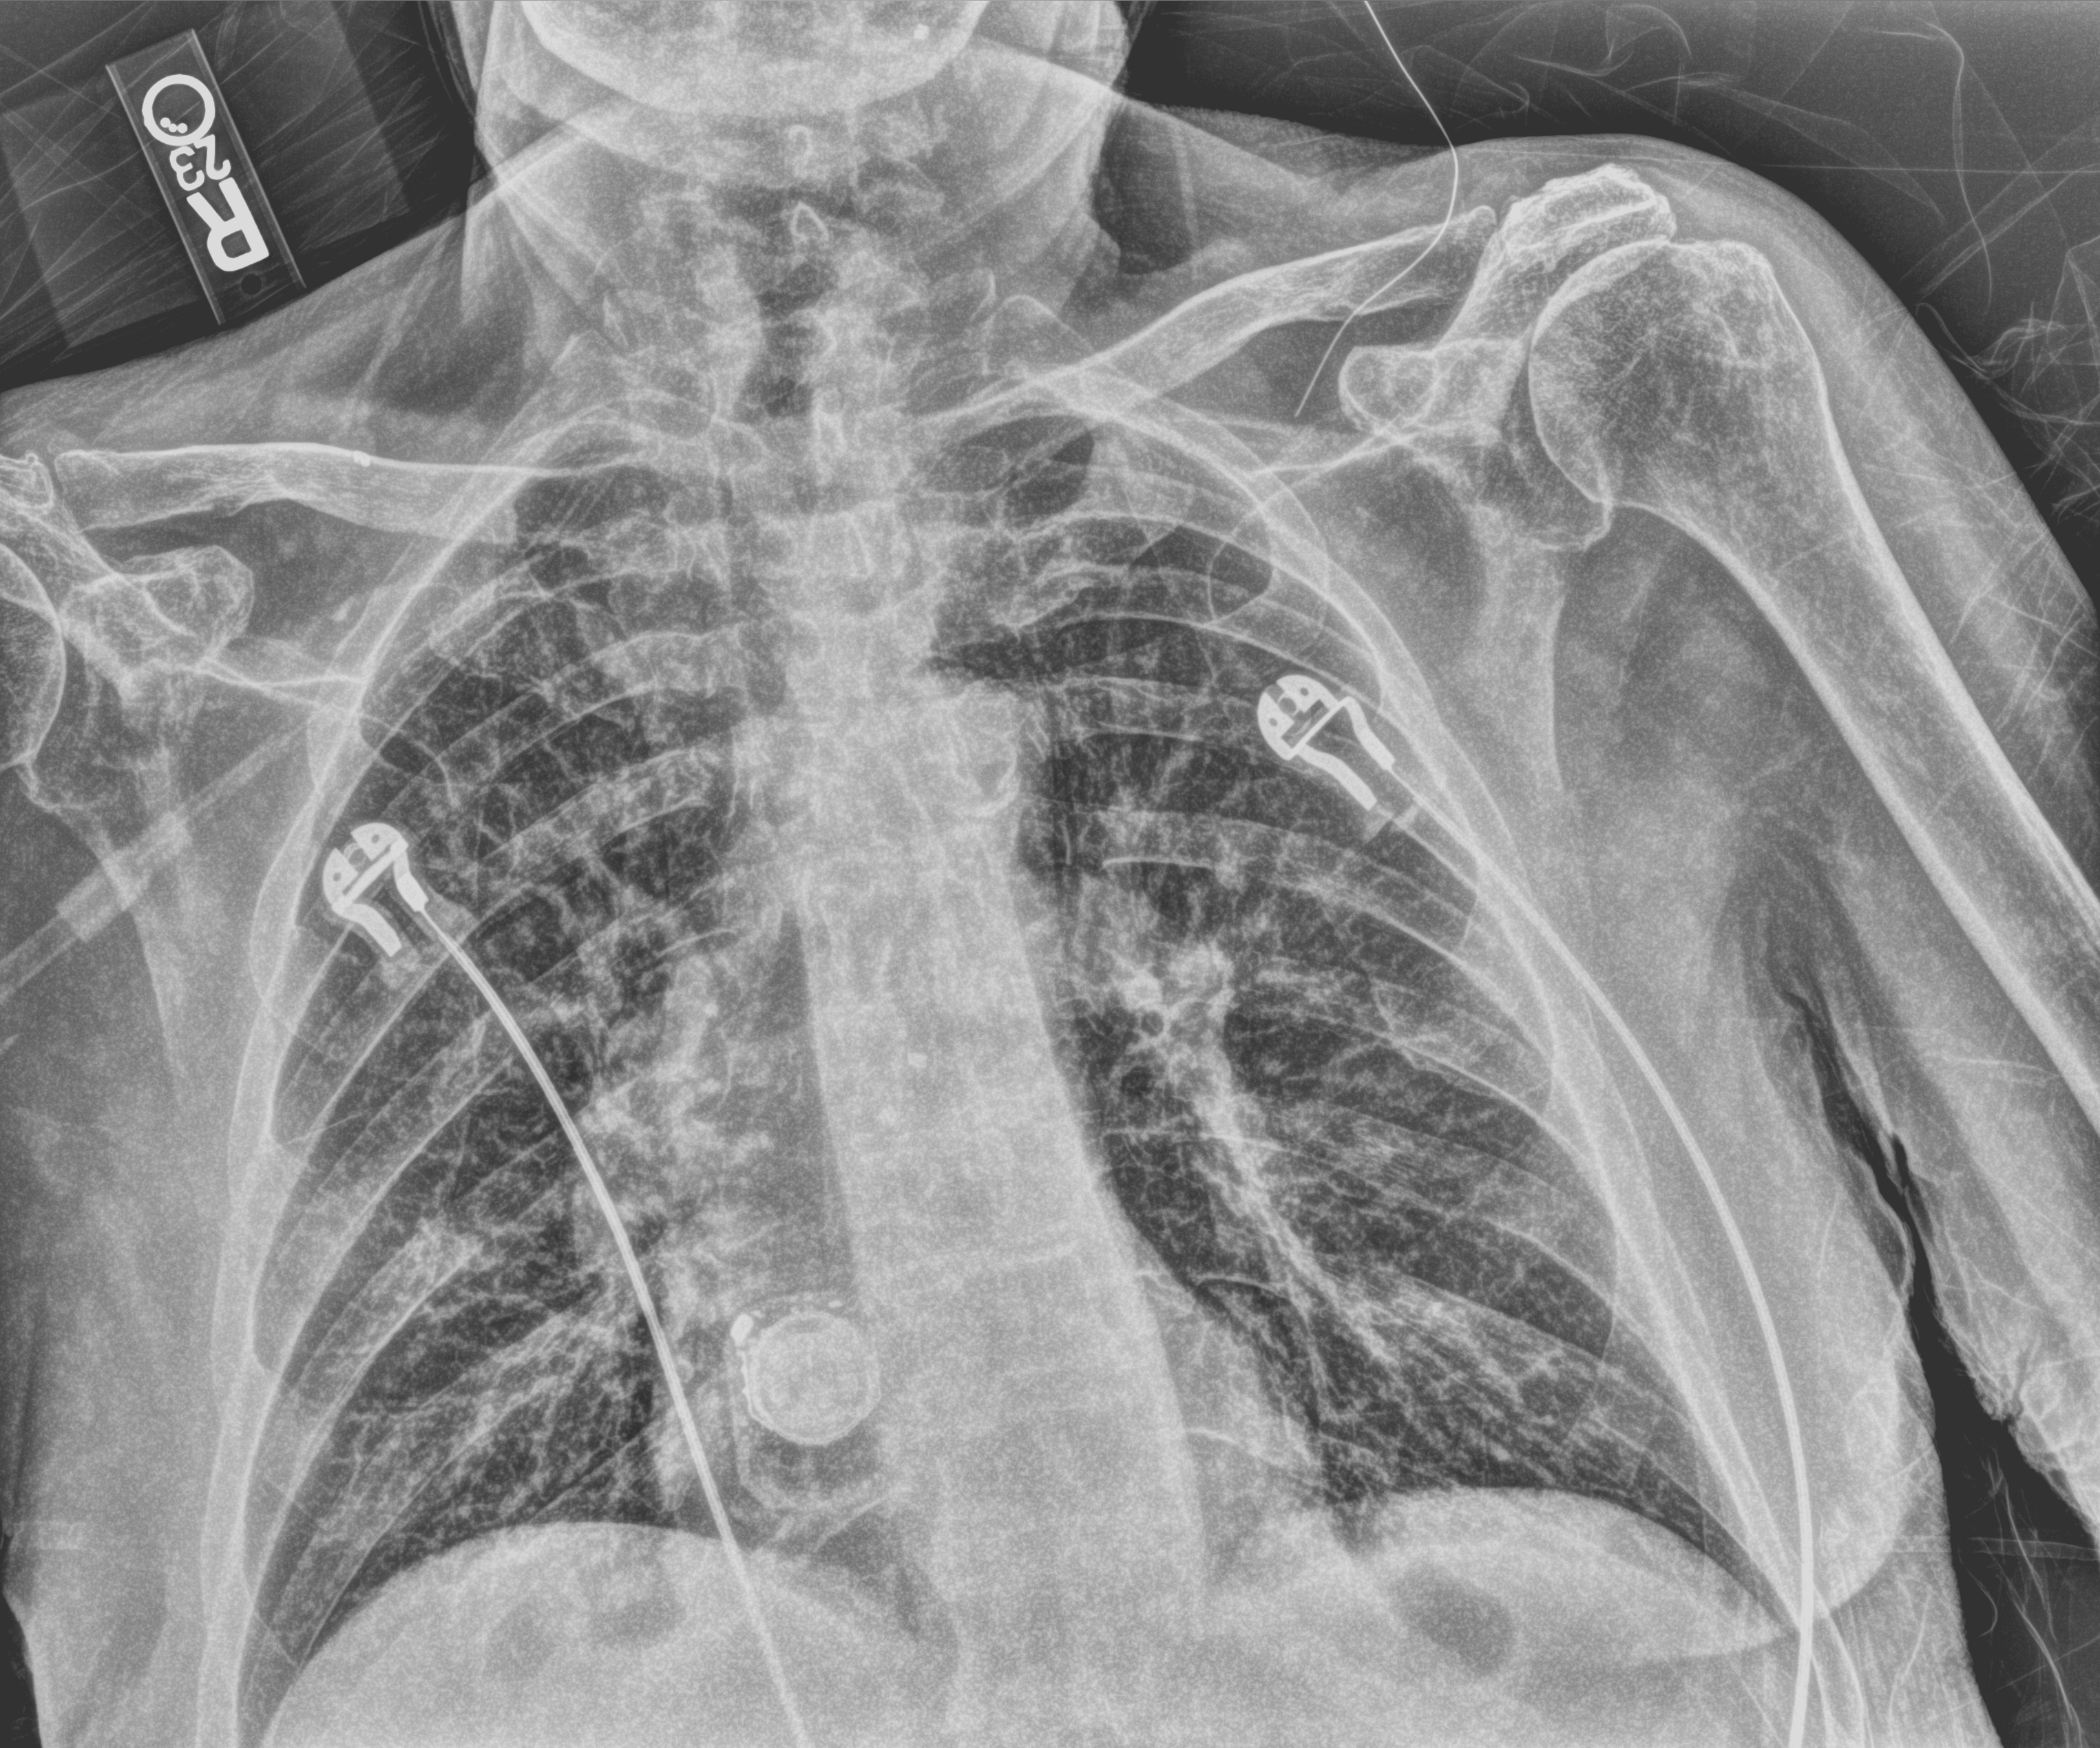
Portable chest radiograph, anteroposterior (AP) projection. Male patient hospitalised with COVID-19, age 75–90 years.
From the hospital-stay record, not from the radiograph (when in the stay this image was taken is not recorded): other chronic lung disease (admission record): no.